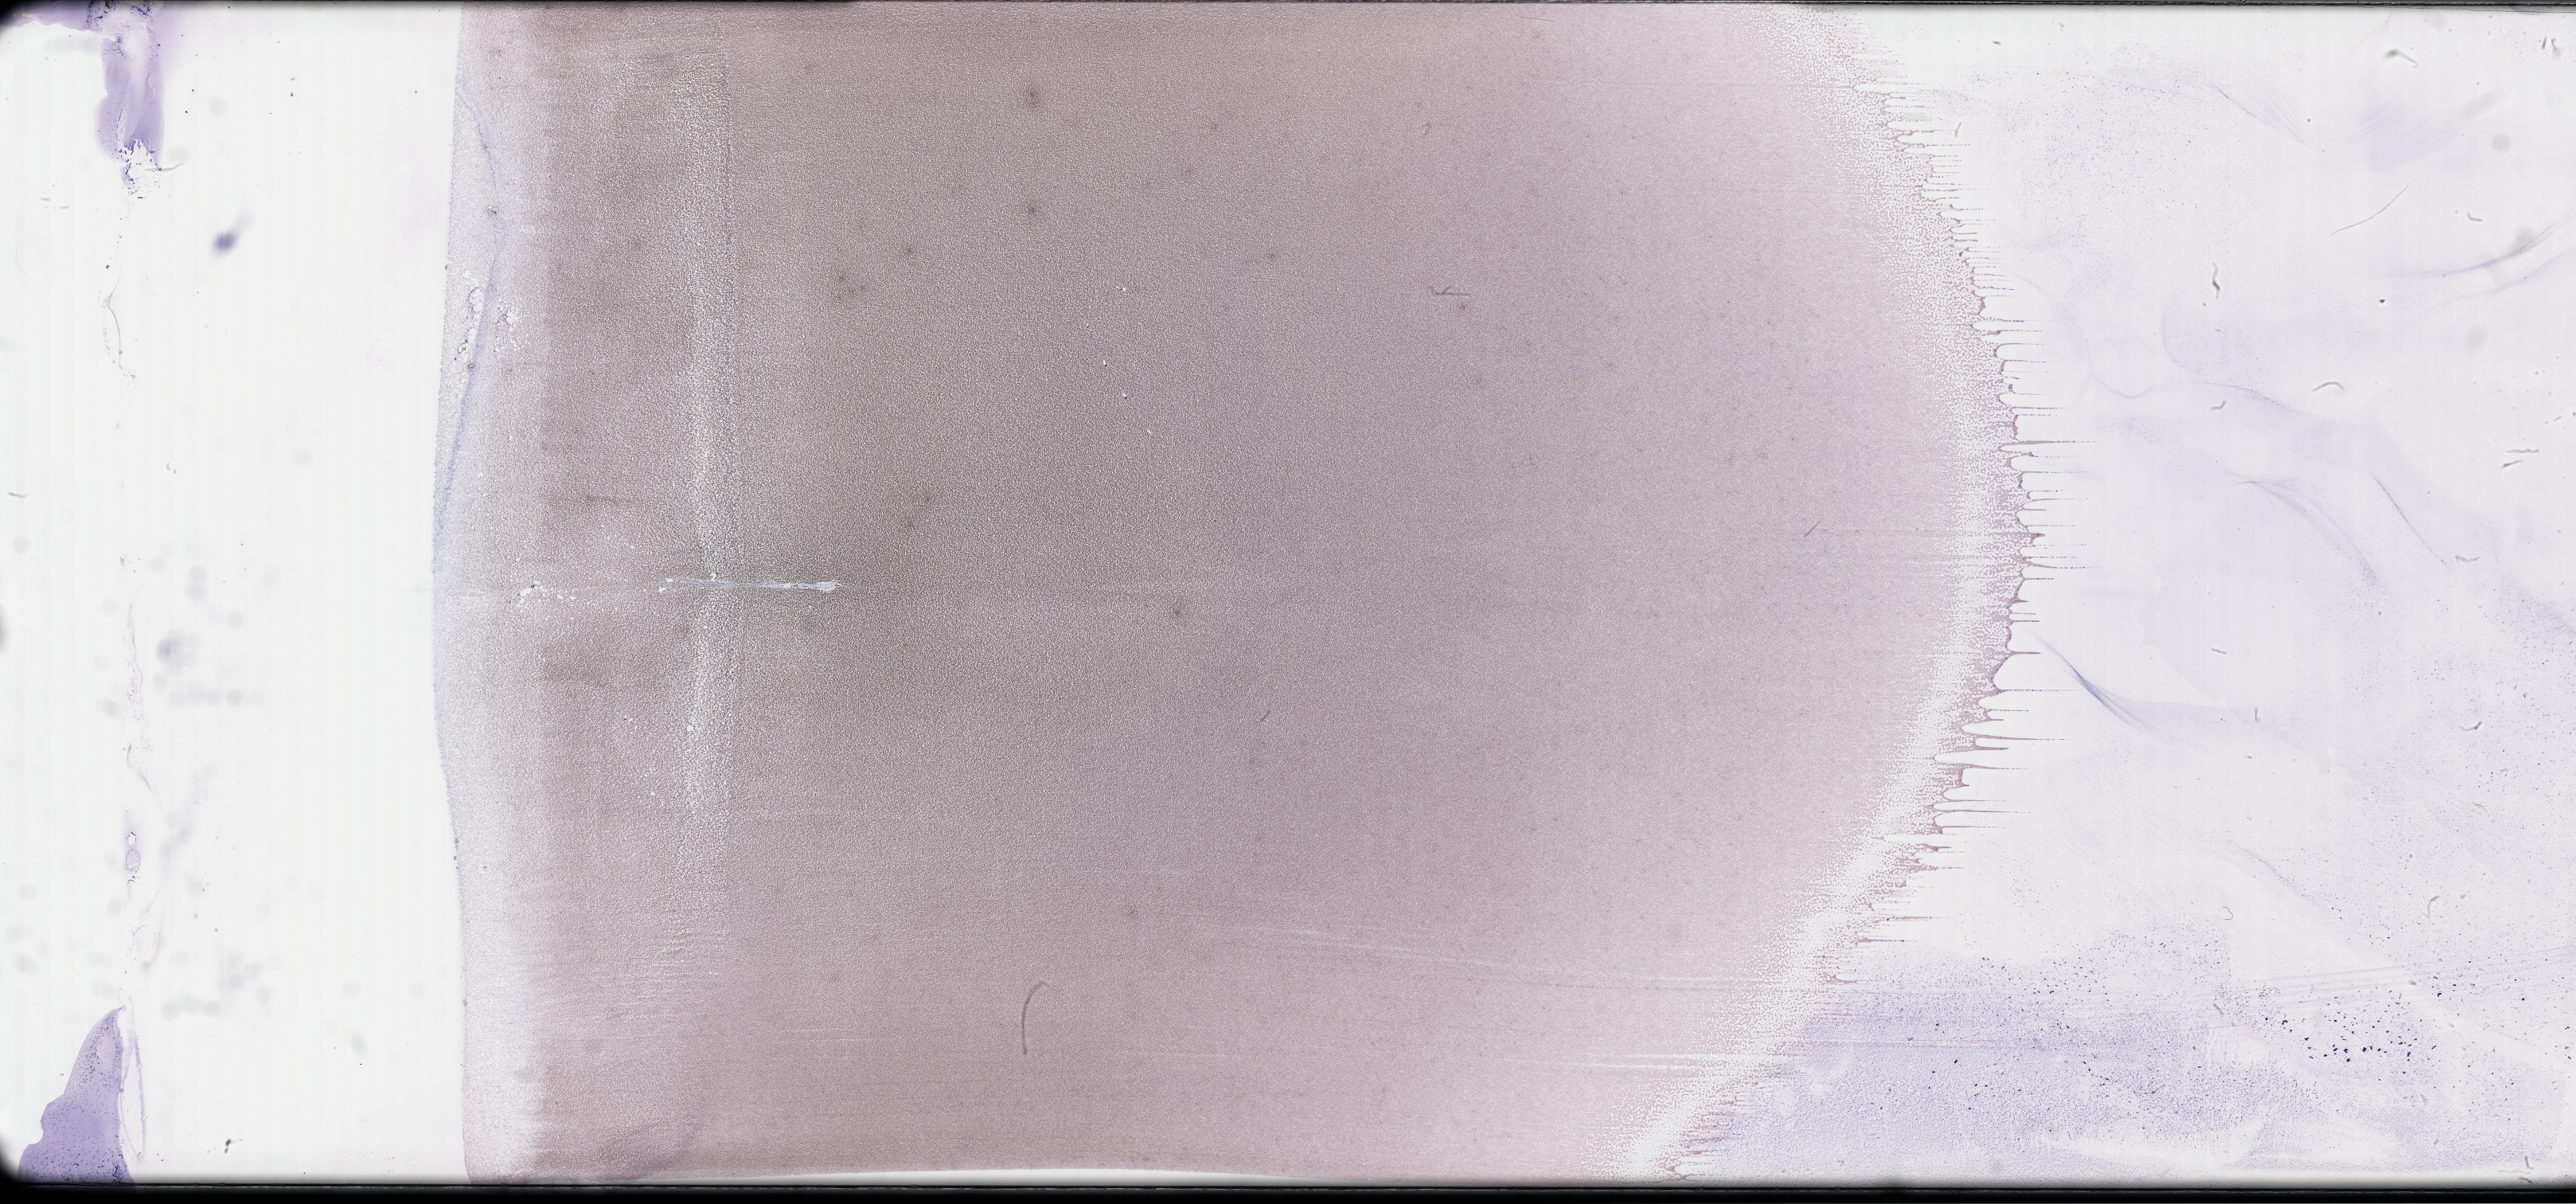
Whole-slide image of a whole blood smear, Wright–Giemsa stain, whole scanned area (about 52.3 x 24.4 mm) shown as a low-resolution overview; smear from an EDTA sample. Patient sex: male.
From a patient with: Plasma Cell Myeloma.